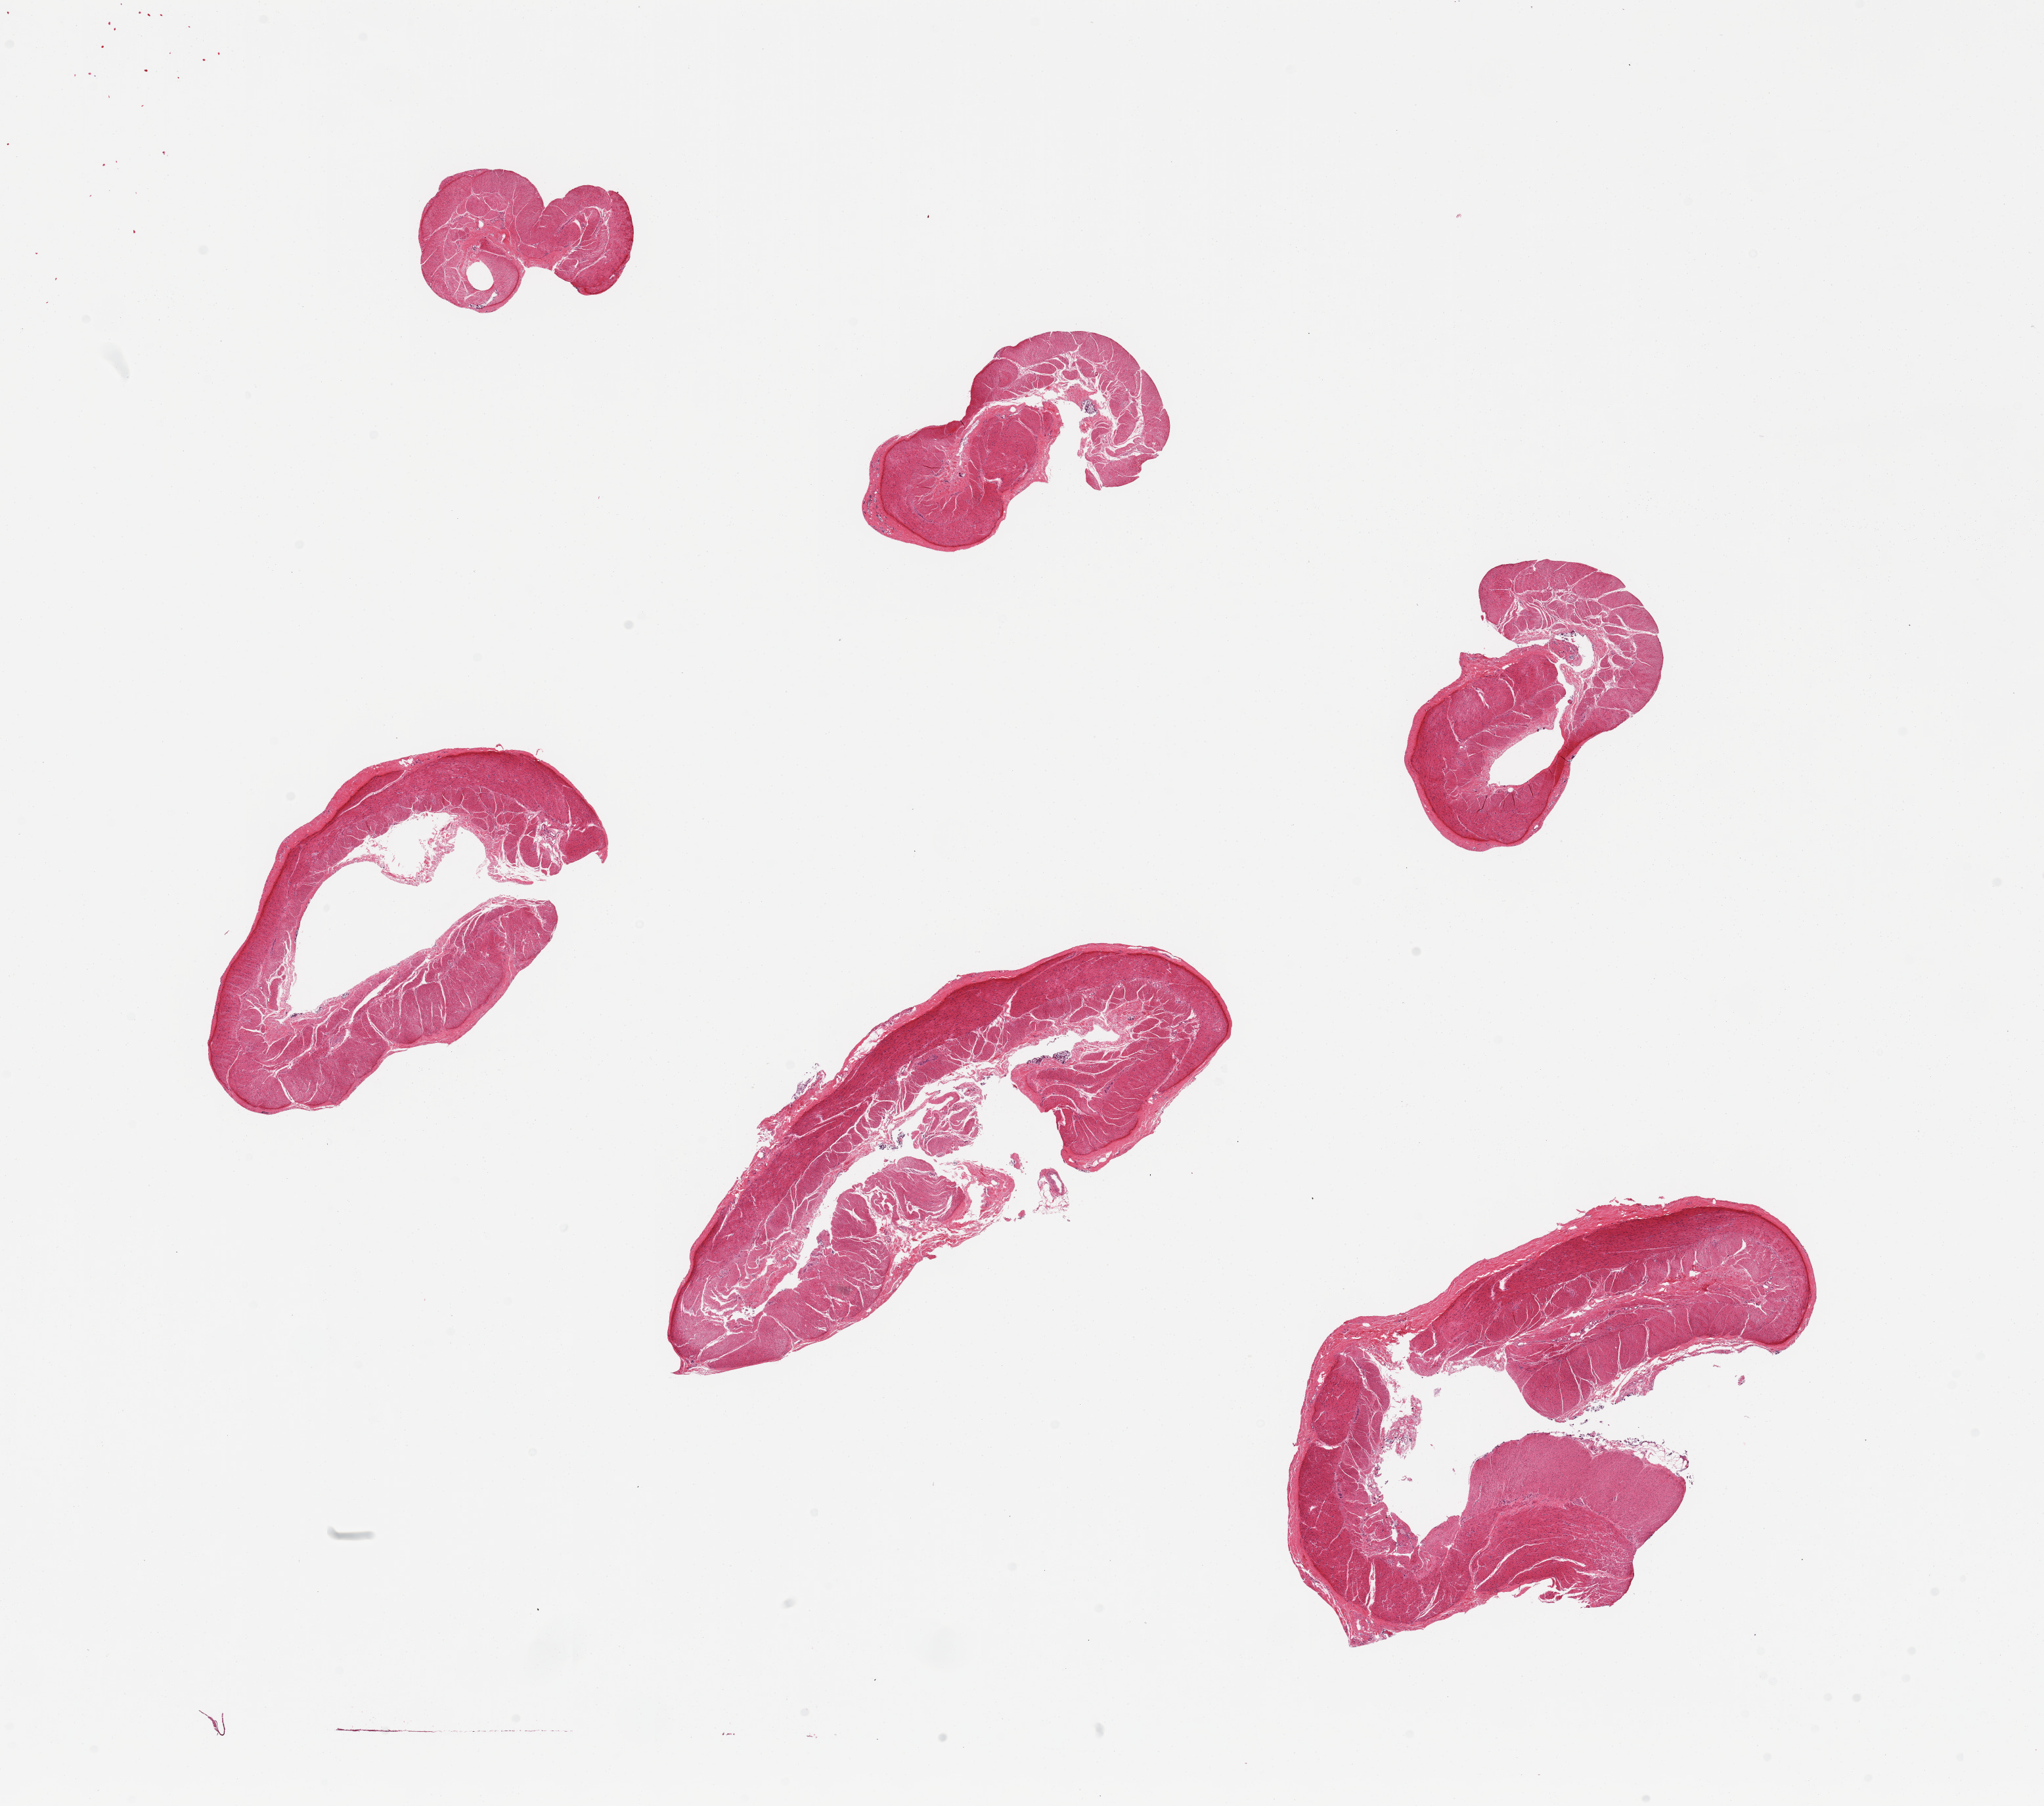
Whole-slide image, haematoxylin and eosin stain, shown as a low-resolution overview of the whole scanned area (about 24.6 x 21.7 mm), PAXgene-fixed paraffin-embedded (PFPE) section, target tissue: transverse colon, tissue donor sample. Male donor.
Review note (as recorded): 6 pieces; muscularis only (this could be sigmoid ).